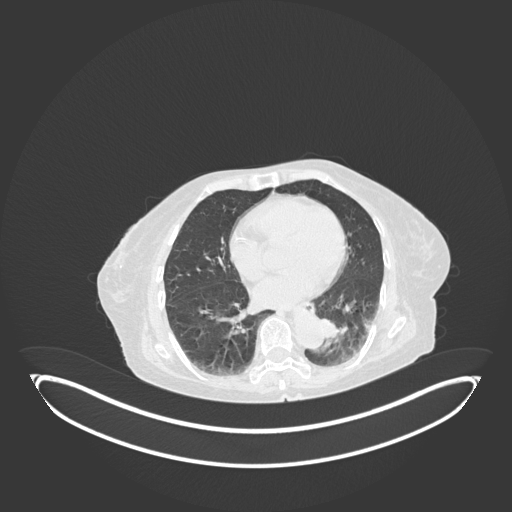
Chest CT, one axial slice; position 39 of 189 along the scan axis; reconstruction kernel B30f; lung window (W 1500 / L -600 HU); 1 mm slice thickness; 512 × 512 image matrix, field of view 500 × 500 mm. Patient: female, 82 years. From the clinical record (not read from this slice): clinical TNM (as recorded): T1b N0 M1.
Structures marked on this image (bounding box drawn by a radiologist):
- lung tumour (recorded histology: adenocarcinoma): bounding box [x1, y1, x2, y2] px = [319, 315, 344, 347]